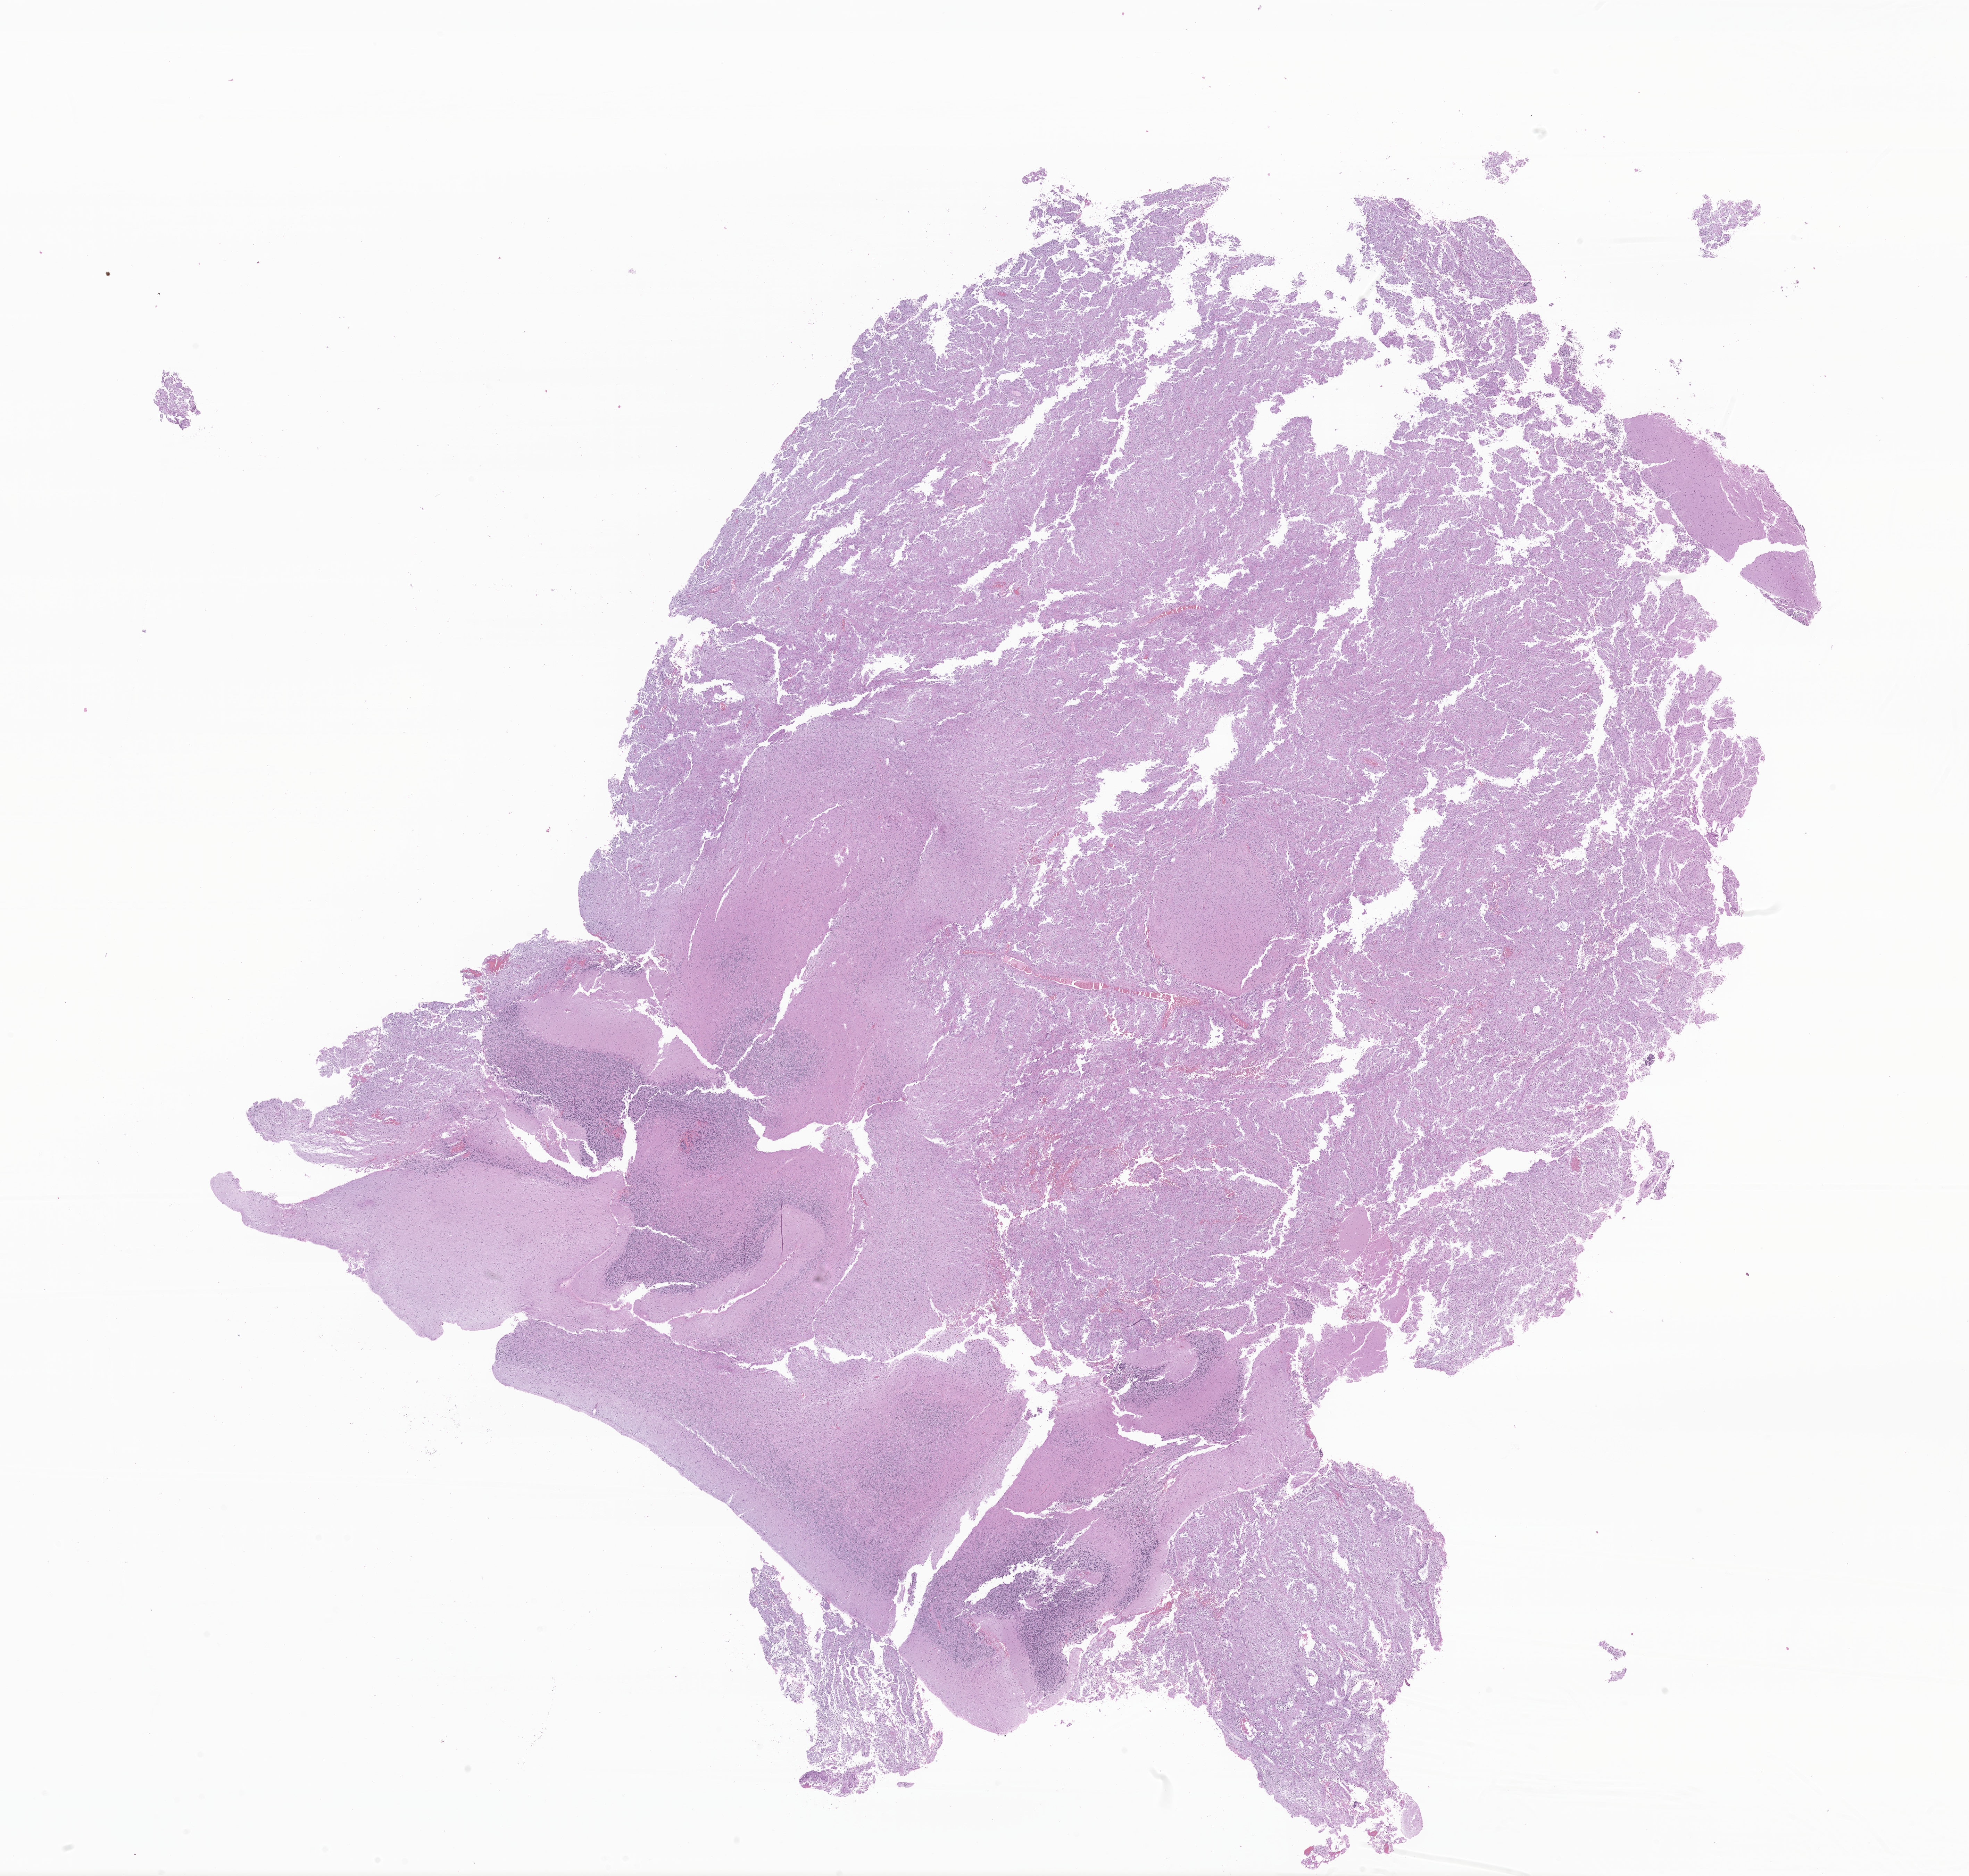
Digitized haematoxylin and eosin-stained section of tumor tissue from the brain — shown as a low-resolution overview of the whole scanned area (about 23.9 x 22.8 mm). FFPE section. Patient female; age 185 months (15 years 5 months).
- recorded diagnosis: Pilocytic astrocytoma